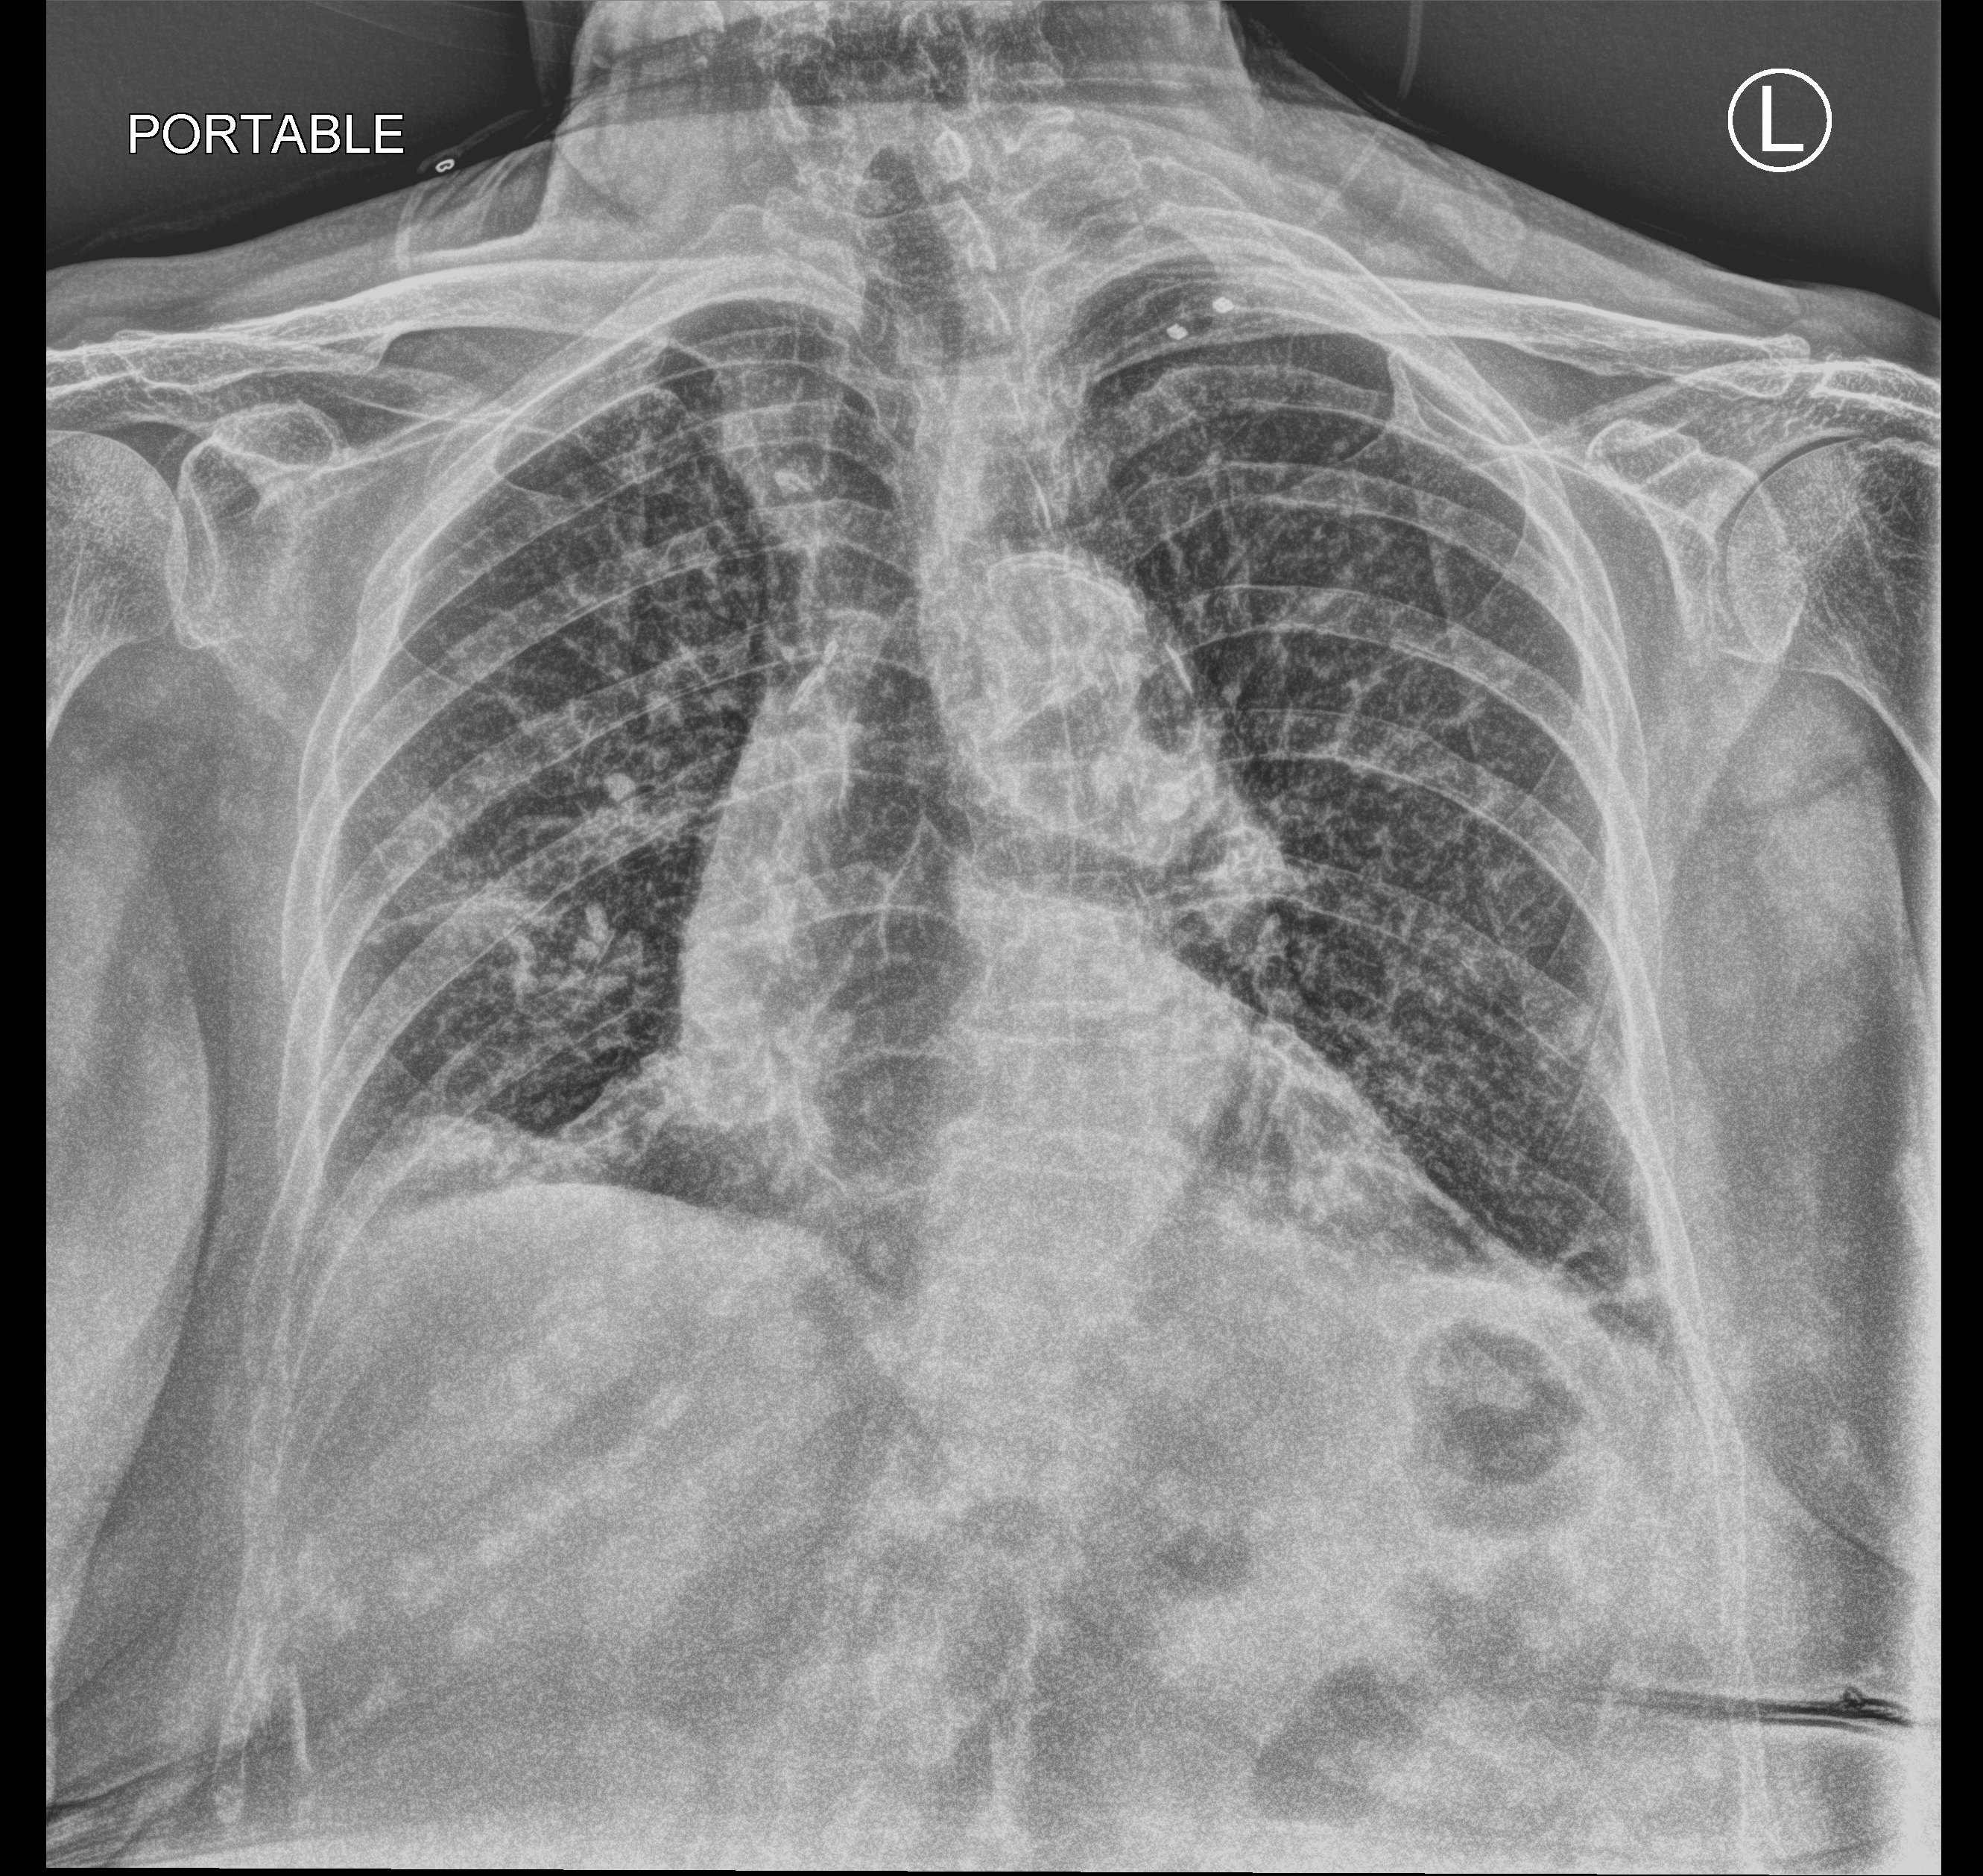
Bedside chest radiograph (computed radiography); anteroposterior (AP) projection. Patient hospitalised with COVID-19; female, aged 75–90 years.
Admission-level facts for this patient (not findings on this image; timing relative to this image not recorded): length of hospital stay: 13 days.